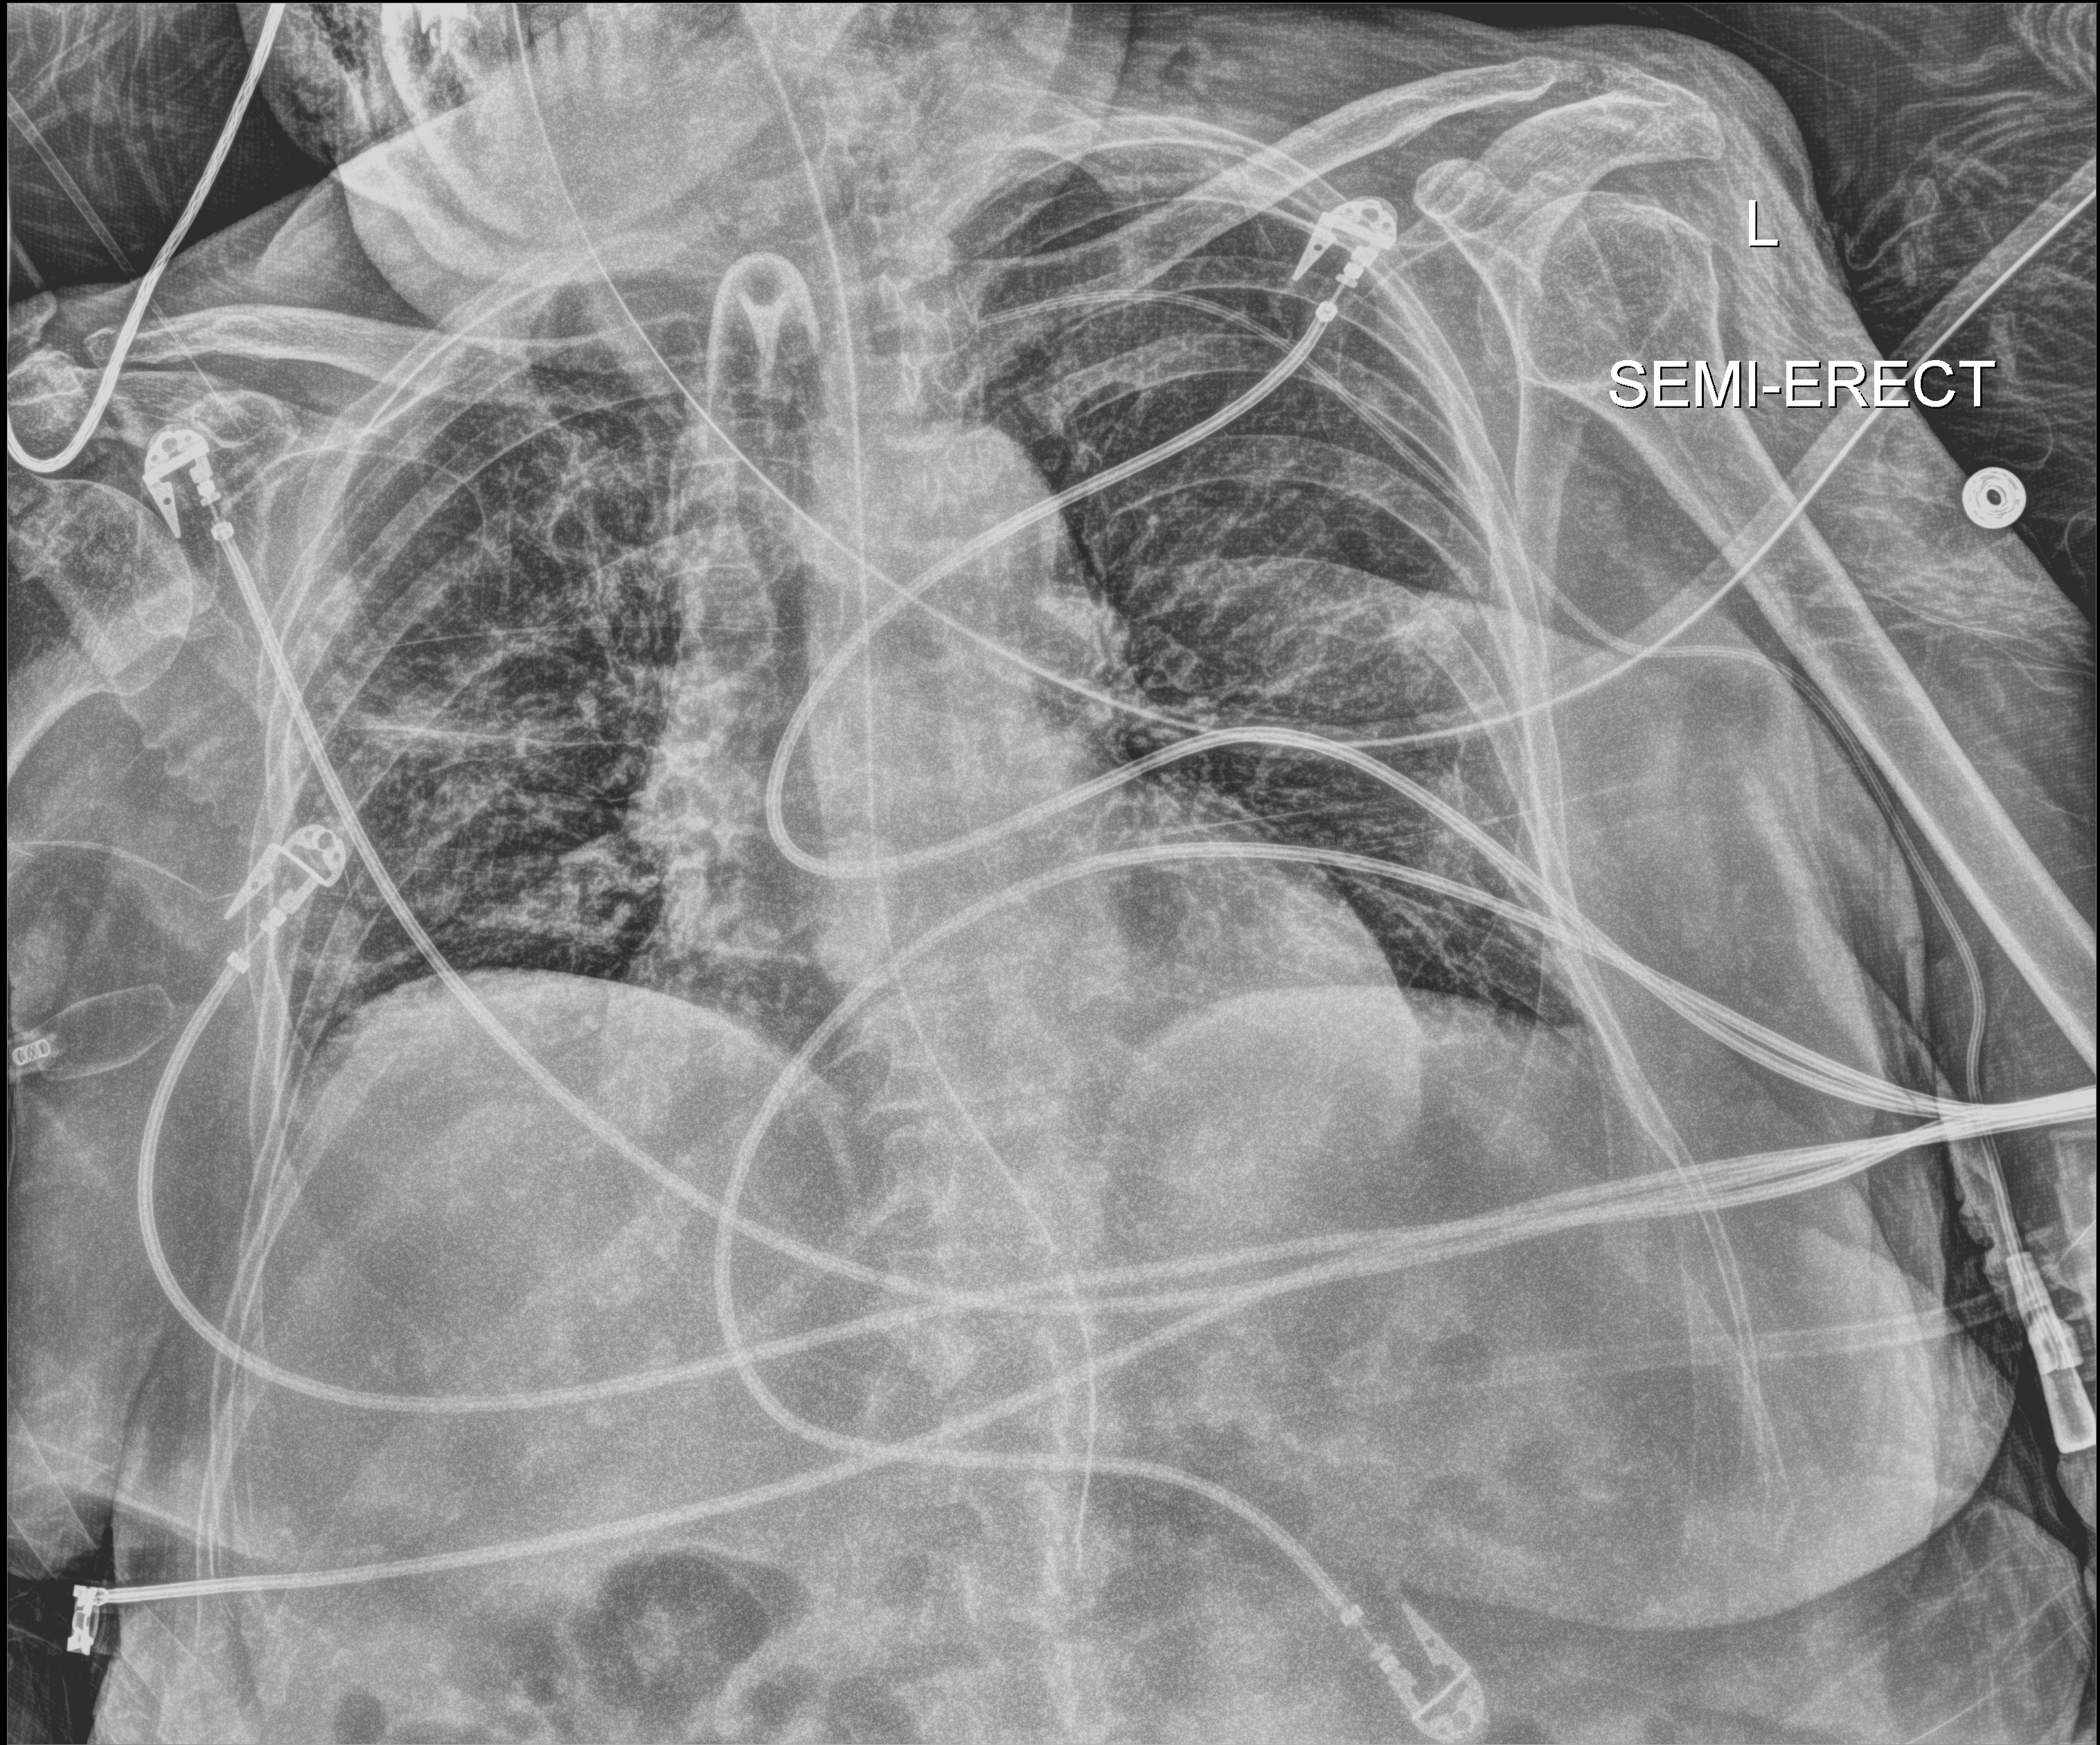
Chest X-ray (portable); anteroposterior (AP) projection. Patient hospitalised with COVID-19; female, aged 75–90 years.
Hospital-stay facts (about this admission, not read from this image; timing relative to this image not recorded):
- mechanically ventilated during this hospital stay: yes